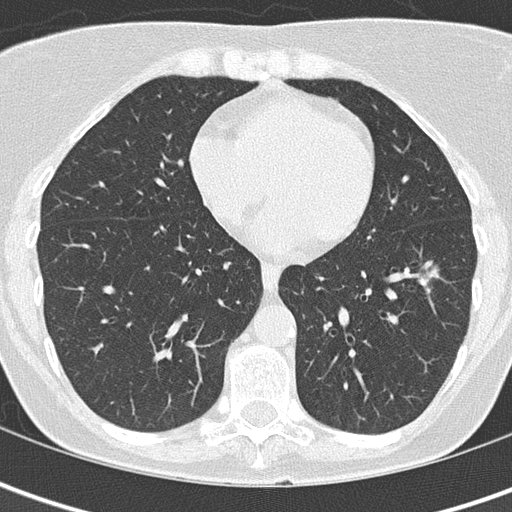
Low-dose screening chest CT, one axial slice; position 57 of 149 along the scan axis; reconstruction kernel B50f; 120 kVp; lung window (W 1500 / L -600 HU); 2 mm slice thickness; 512 × 512 image matrix, field of view 280 × 280 mm.
Structures marked on this image (manually delineated by an expert):
- lesion 1 (tumor, lower lobe of left lung): bounding box <419,264,437,285> (left, top, right, bottom; pixels)